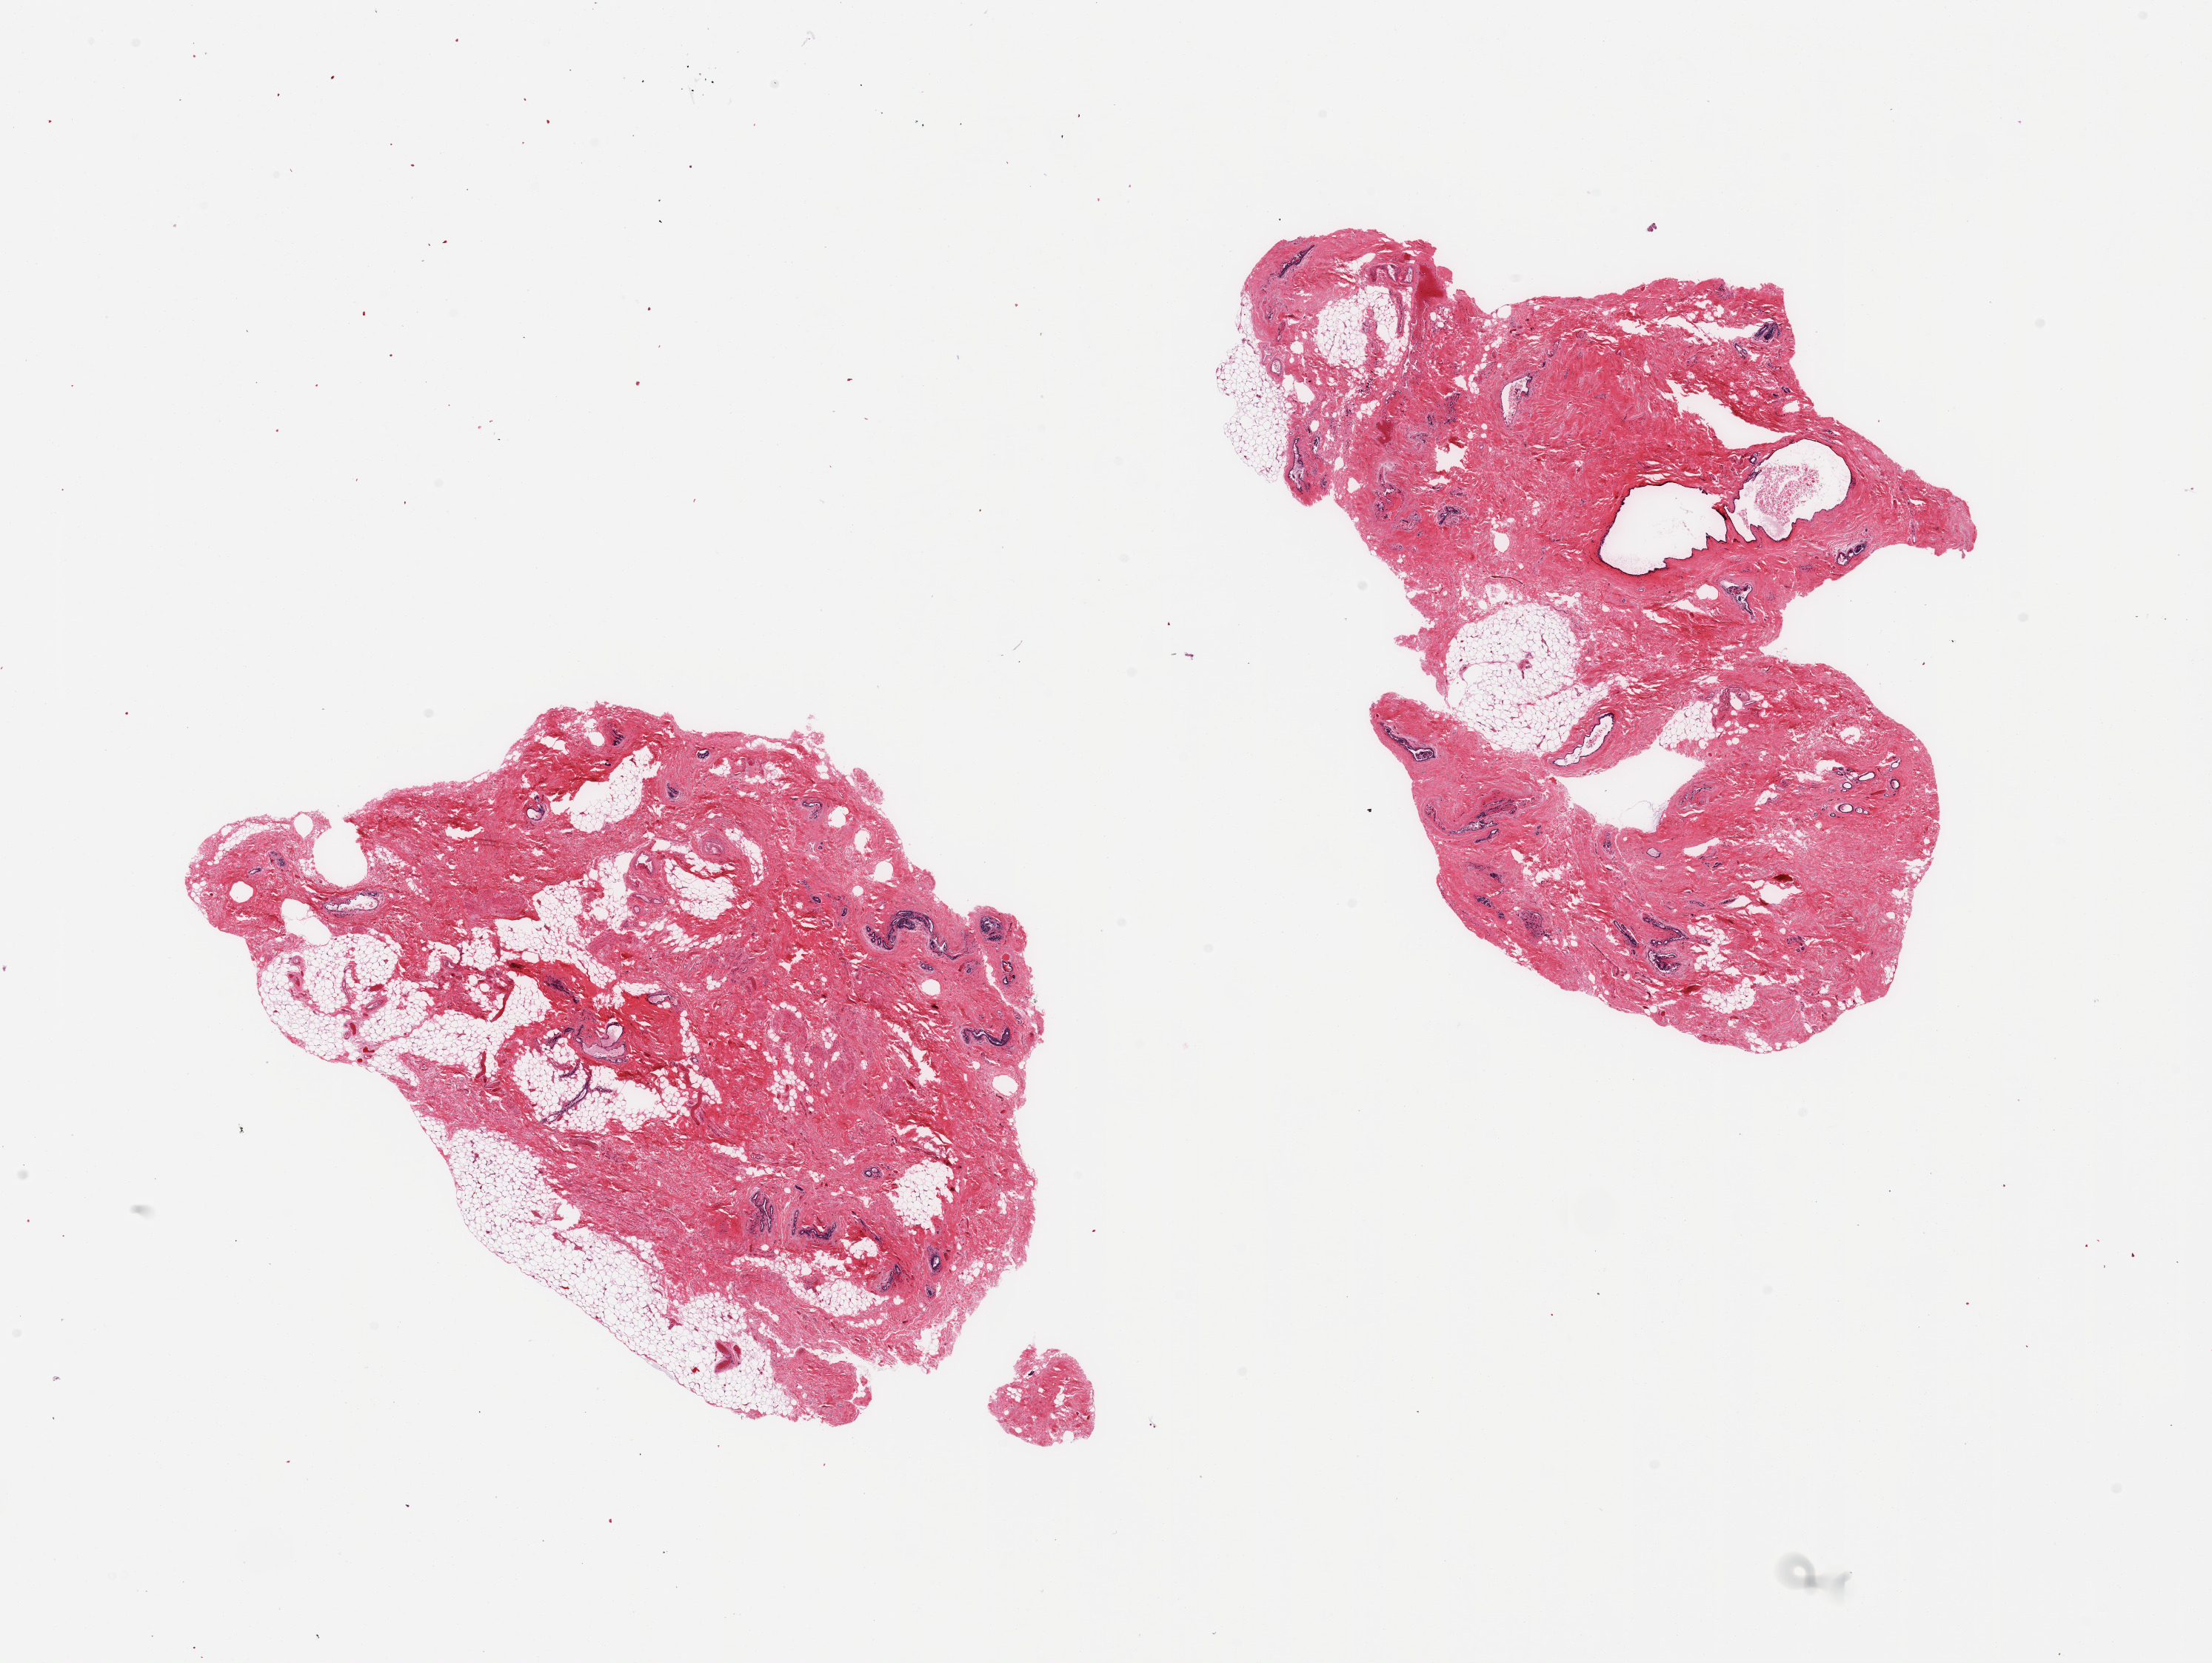
Whole-slide image, H&E stain, a low-resolution overview of the entire scanned area, about 23.6 x 17.8 mm (from a 20x scan), PAXgene-fixed paraffin-embedded (PFPE) section, target tissue: breast, tissue donor sample.
Review note (as recorded): 2 pieces; atrophic mammary tissue with focal fibrocystic changes.